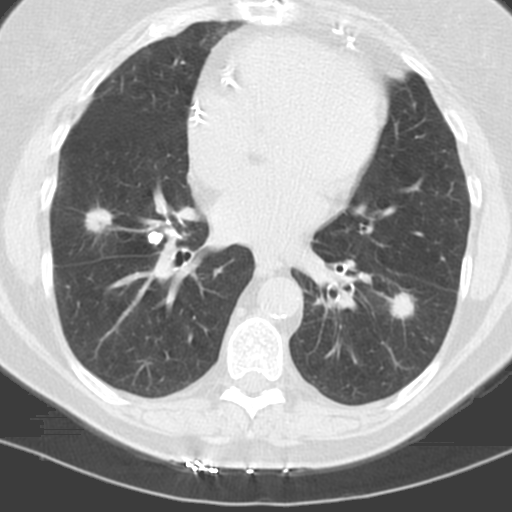
Low-dose screening chest CT, one axial slice. Slice 49 of 121 in the series (ordered by position). 120 kVp. Lung window (W 1500 / L -600 HU). 3.2 mm slice thickness. 512 × 512 image matrix, field of view 278 × 278 mm.
Annotated regions visible in this slice (manually delineated by an expert):
- lesion 1 (tumor, lower lobe of left lung): bounding box (x1, y1, x2, y2) in pixels: (390, 293, 415, 319)
- lesion 3 (tumor, middle lobe of right lung): (86, 209, 112, 232)